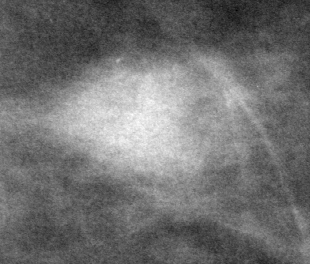
Cropped region of a digitized screen-film mammogram centred on a radiologist-marked abnormality; left breast; CC view.
- Mass, shape oval, margins microlobulated; BI-RADS assessment category 4; subtlety rating 5 on a 1 (subtle) to 5 (obvious) scale; pathology result (as recorded, not read from the image): malignant.